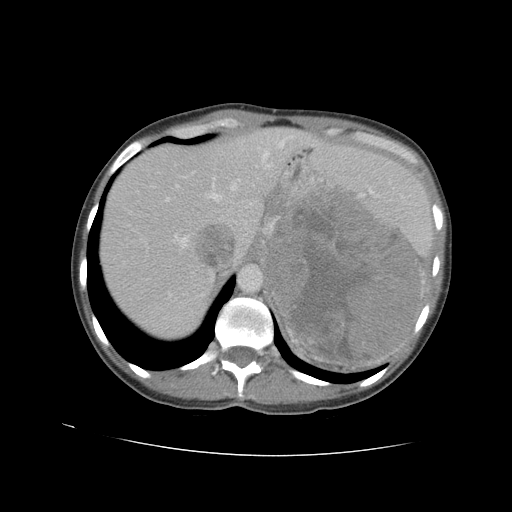
Contrast-enhanced abdominal CT, one axial slice; reconstruction kernel STANDARD; 120 kVp; intravenous contrast given; soft-tissue window (W 400 / L 40 HU); 512 × 512 image matrix, field of view 360 × 360 mm. Female patient. From the clinical record (not read from this slice): diagnosis: adrenocortical carcinoma; tumour side: left adrenal; tumour size at pathology: 18 cm; Ki-67 index: 11 %; stage (as recorded): 3.
Annotated regions visible in this slice (semi-automatically segmented with operator editing):
- mass: bounding box <266,193,419,363> (left, top, right, bottom; pixels)